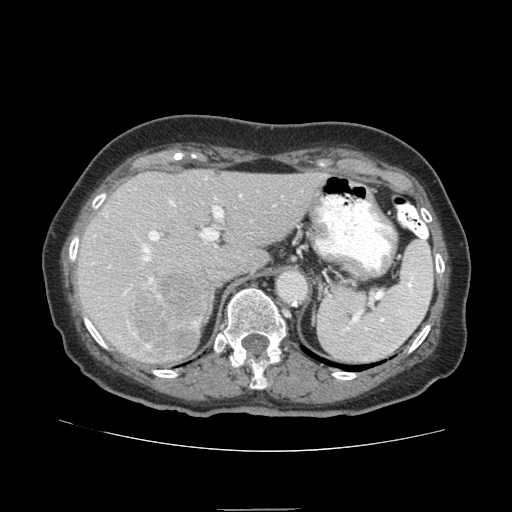
Contrast-enhanced abdominal CT (liver protocol), one axial slice. Position 53 of 95 along the scan axis. Reconstruction kernel STANDARD. 140 kVp. Soft-tissue window (W 400 / L 40 HU). 512 × 512 image matrix. Case-level facts recorded for this patient, not image findings: diagnosis: hepatocellular carcinoma (patient treated with transarterial chemoembolisation; whether this scan precedes or follows treatment is not stated here); TNM stage (as recorded): Stage-IVA; Child-Pugh class: B; tumour differentiation: moderately differentiated.
Outlined on this slice (semi-automatic segmentation, software-assisted and operator-edited):
- liver parenchyma outside the tumour (the mass and vessels are separate outlines, so this box may not span the whole liver): bounding box <76,170,327,364> (left, top, right, bottom; pixels)
- mass: <129,273,210,356>
- liver vessels: <124,195,242,348>